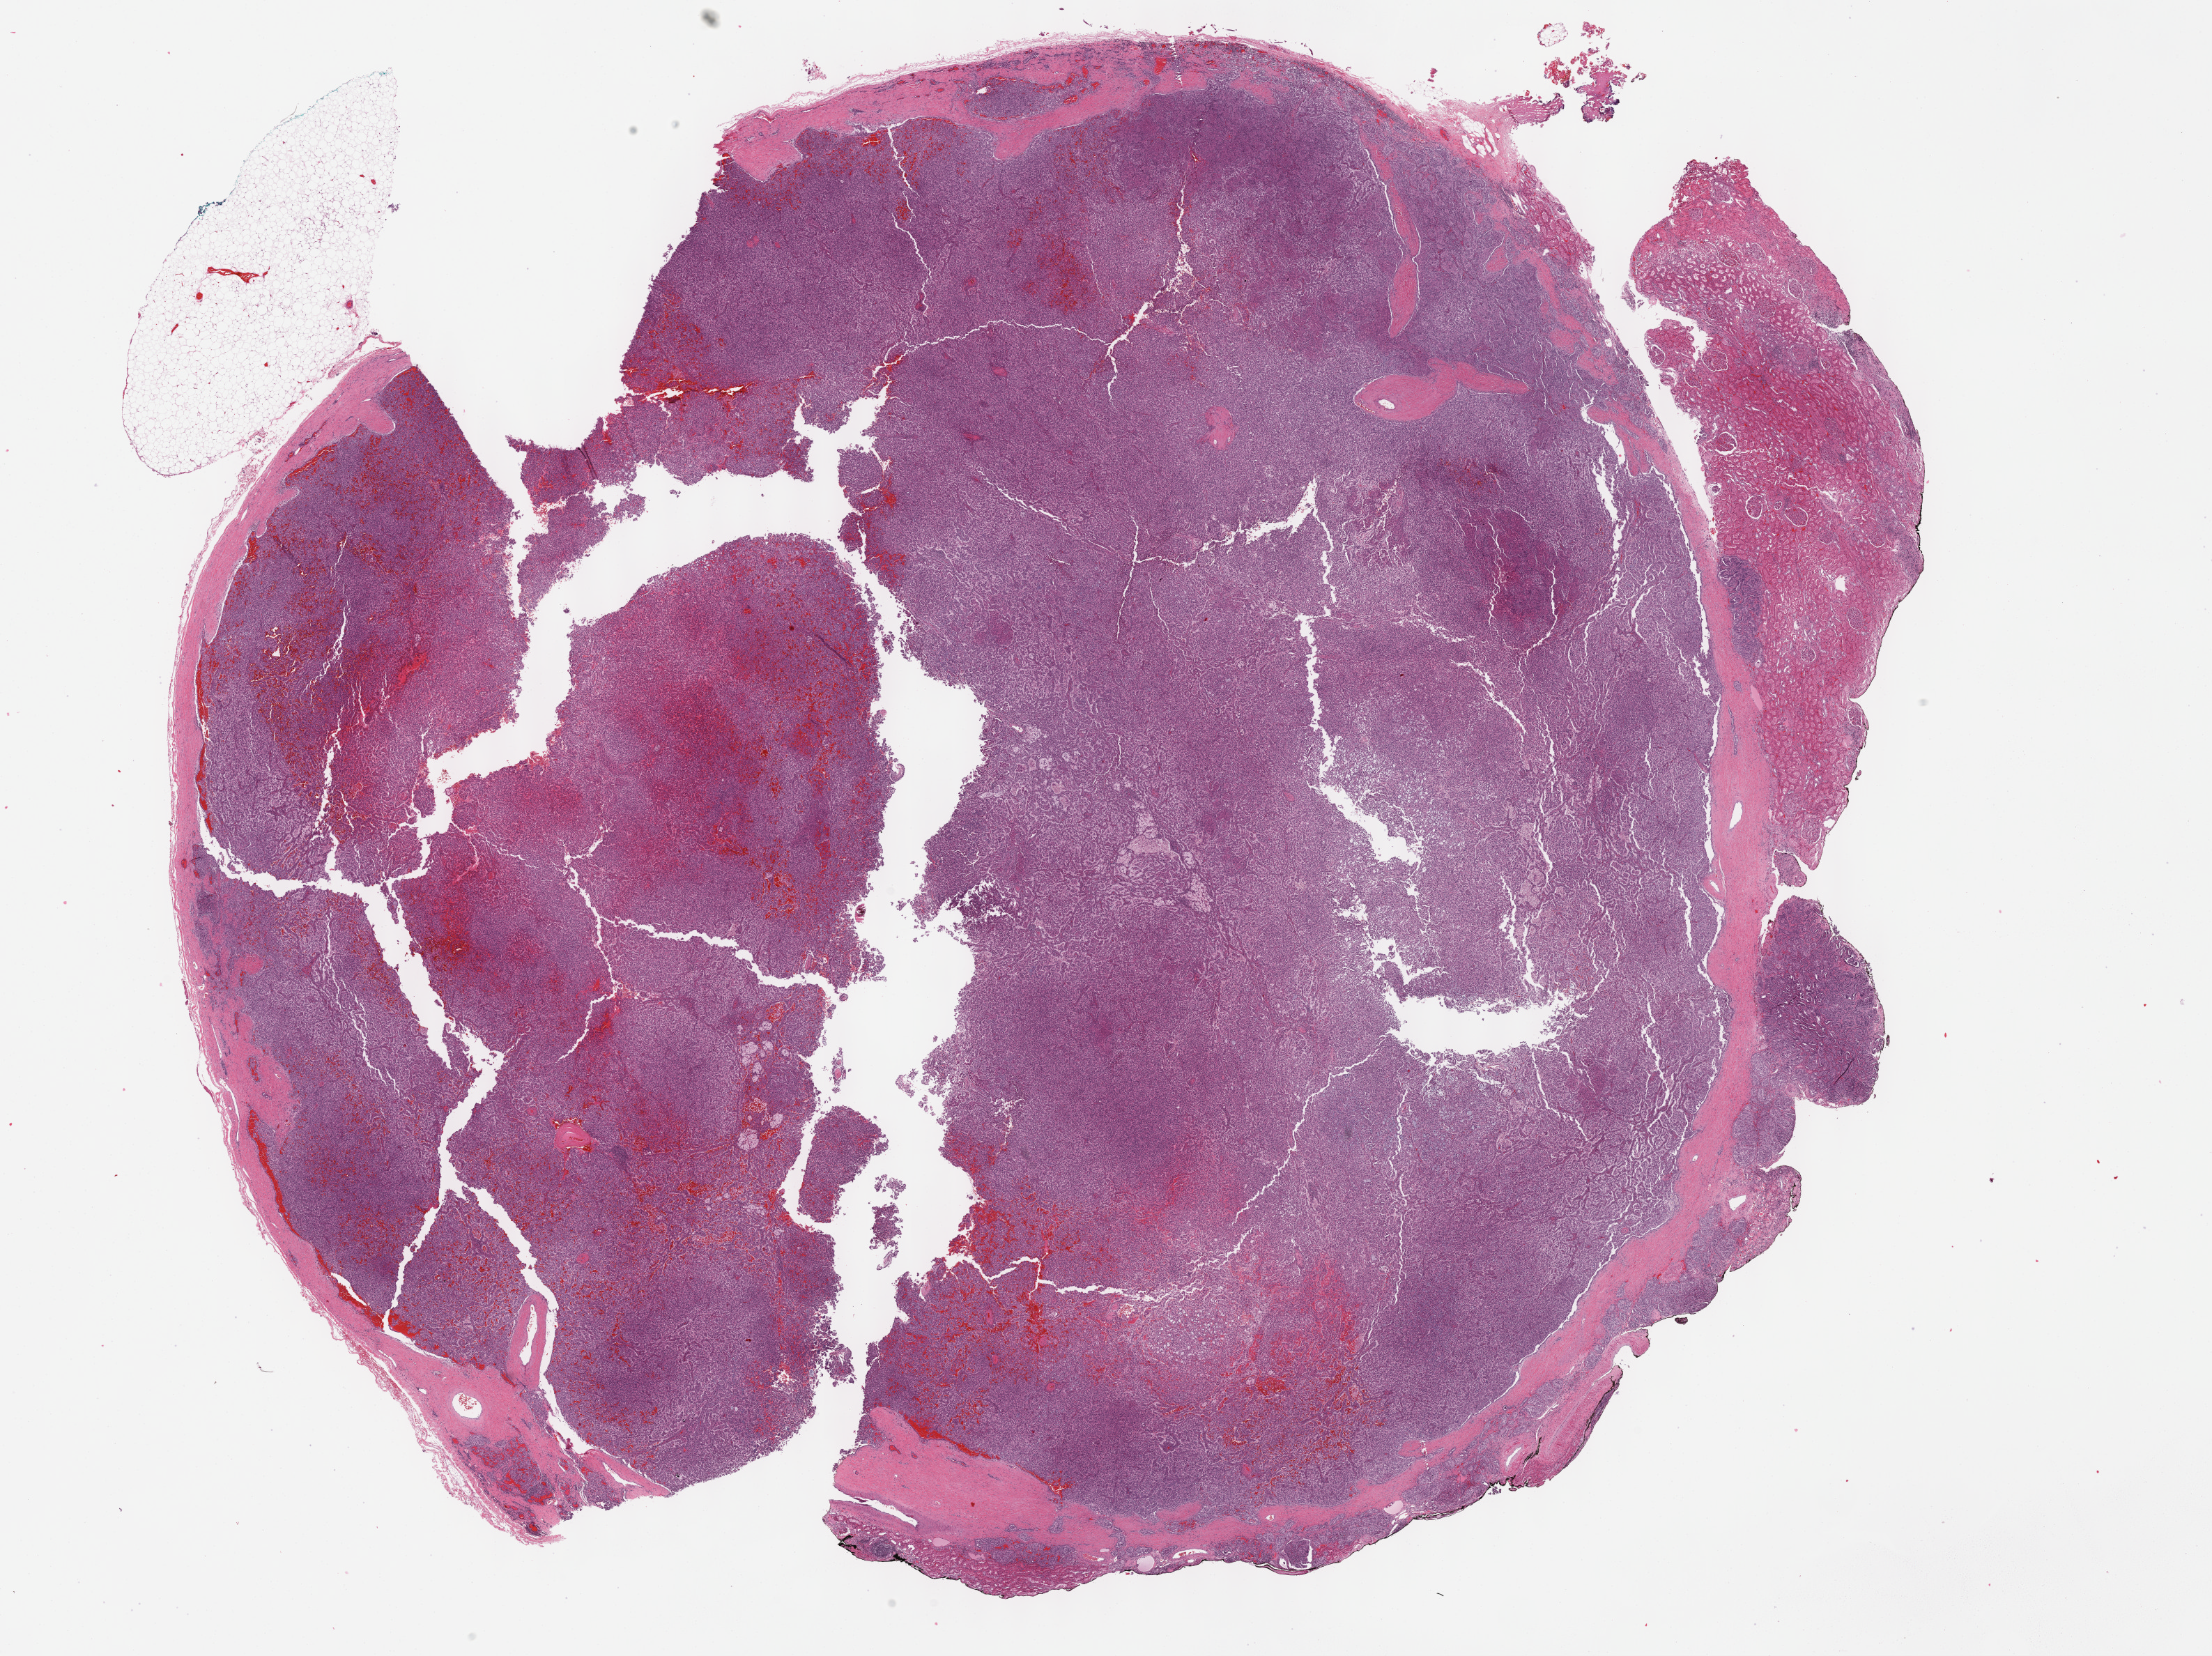
Digitized Hematoxylin and eosin (H&E) stained tissue section (whole slide), whole scanned area (about 25.7 x 19.2 mm) shown as a low-resolution overview, FFPE section, sample: primary tumour, kidney. Male patient; age at initial diagnosis 44 years.
Histologic diagnosis: Papillary adenocarcinoma, NOS. Laterality: left. AJCC pathologic stage: I (7th edition).